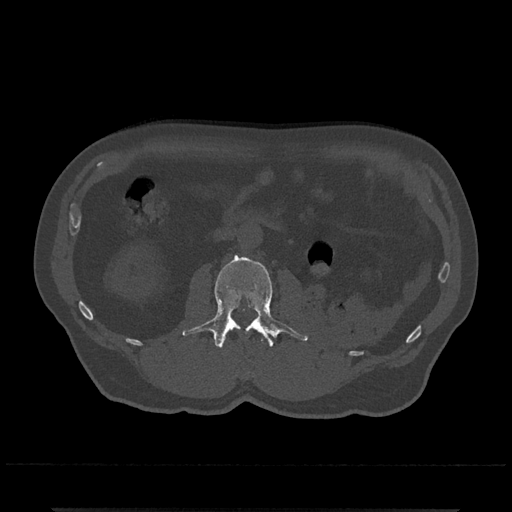
CT including the spine, one axial slice; slice 298 of 797 in the series (ordered by position); 120 kVp; bone window (W 1800 / L 400 HU); 0.5 mm slice thickness; 512 × 512 image matrix, field of view 393 × 393 mm. Patient: male, 67 years. From the clinical record (not read from this slice): primary cancer: prostate.
Outlined on this slice (semi-automatically segmented with operator editing):
- L2 vertebra: bounding box <182,255,309,348> (left, top, right, bottom; pixels)